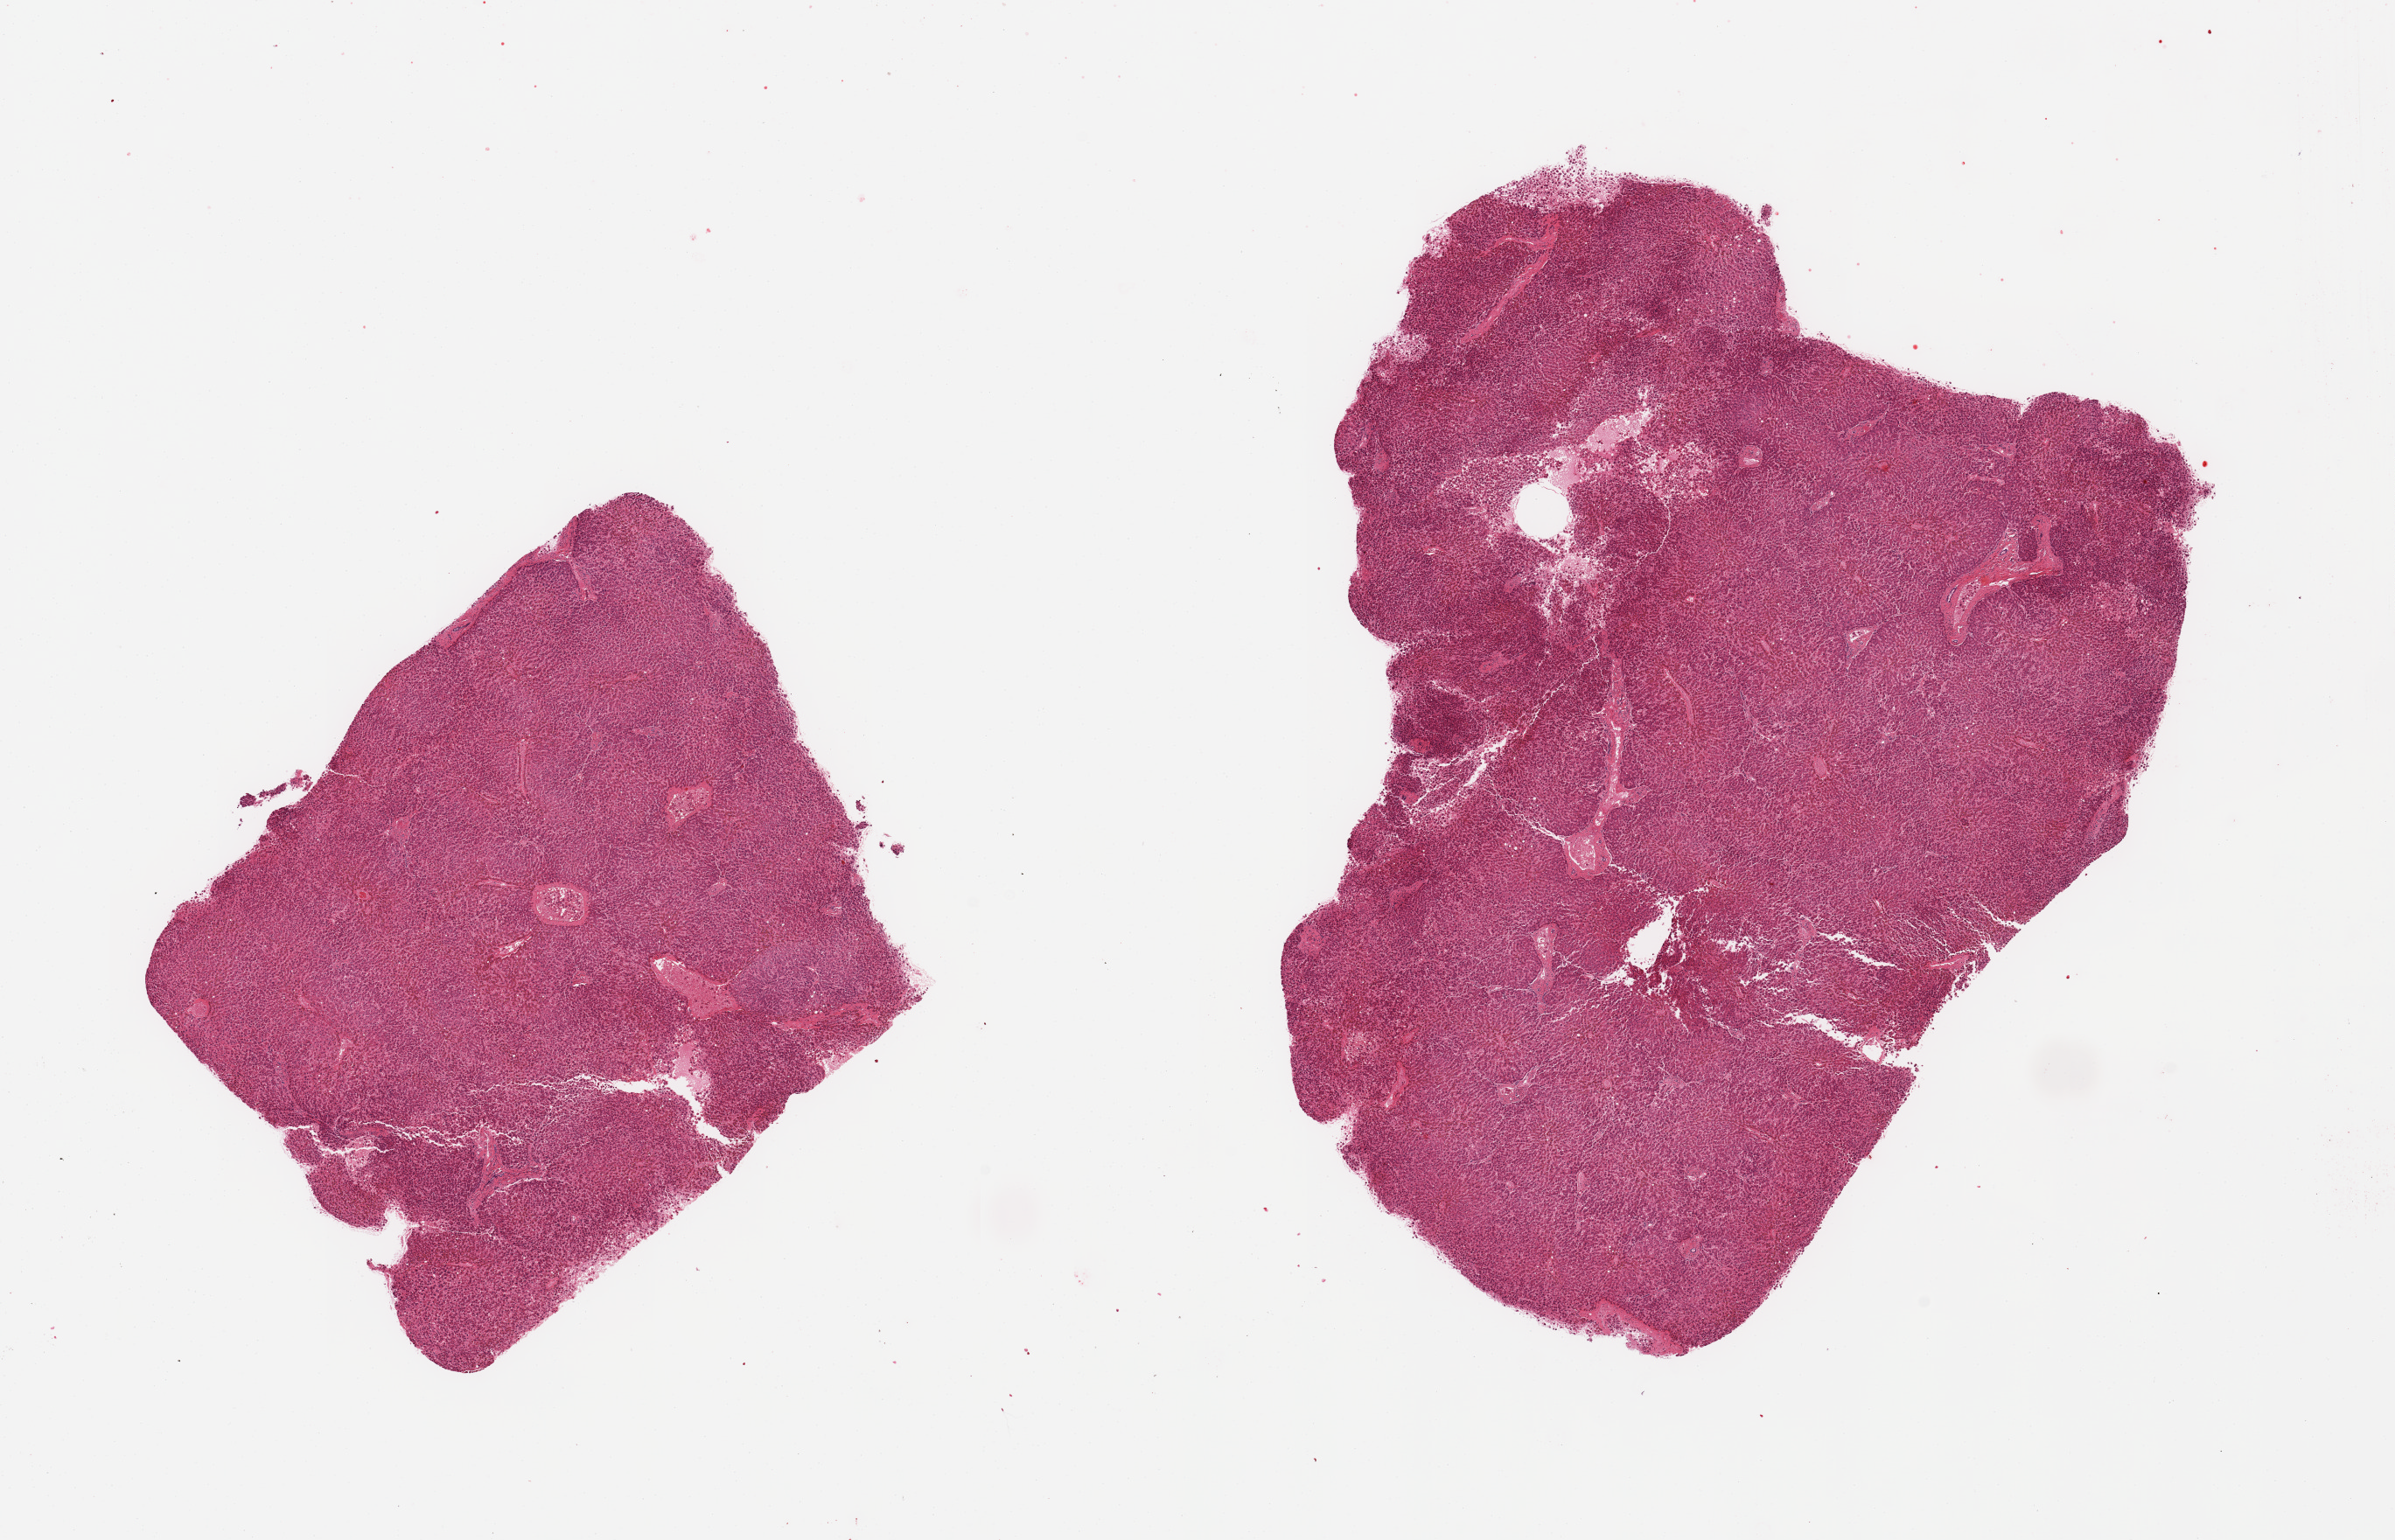
Hematoxylin and eosin (H&E) whole-slide image, shown as a low-resolution overview of the whole scanned area (about 21.7 x 13.9 mm). PAXgene-fixed paraffin-embedded (PFPE) section. Section of liver (target tissue). Donor tissue sample. Male donor.
Reviewer comment on this tissue sample: 2 pieces, mild macrovesicular steatosis, passive chronic congestion.